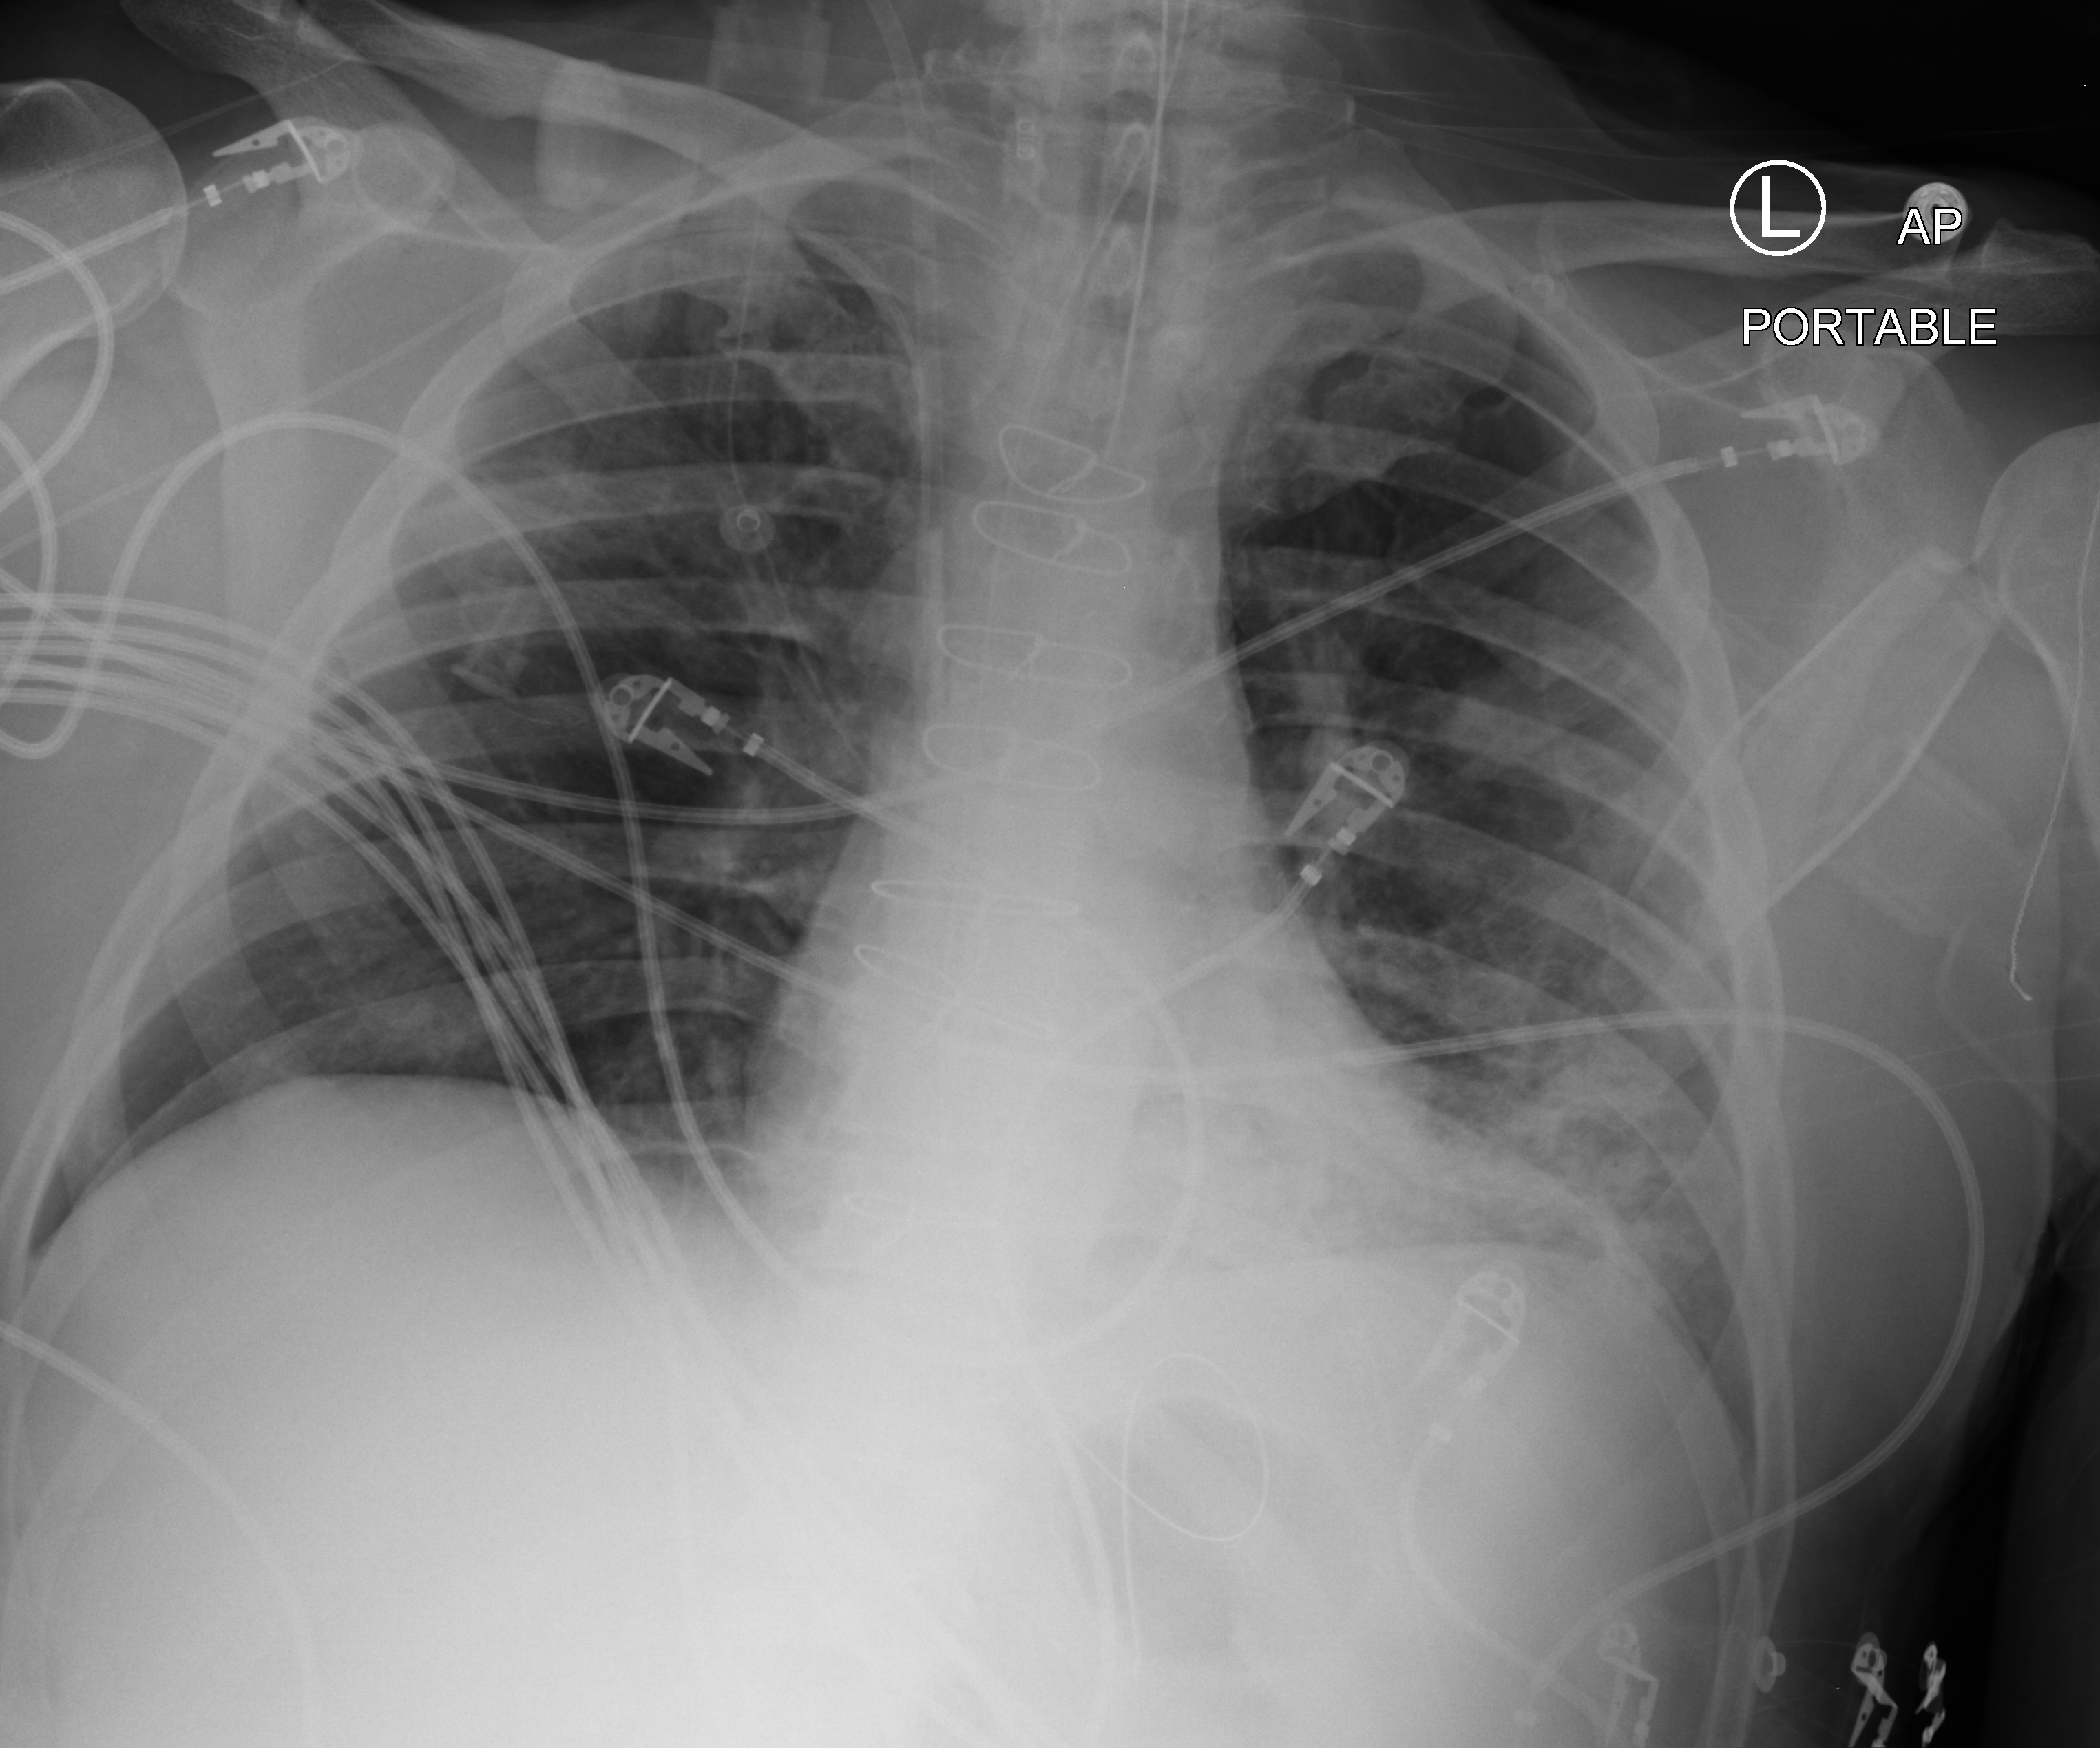
Bedside chest radiograph (computed radiography). Male patient hospitalised with COVID-19, age 60–74 years.
Admission-level facts for this patient (not findings on this image; timing relative to this image not recorded): length of hospital stay: 44 days.